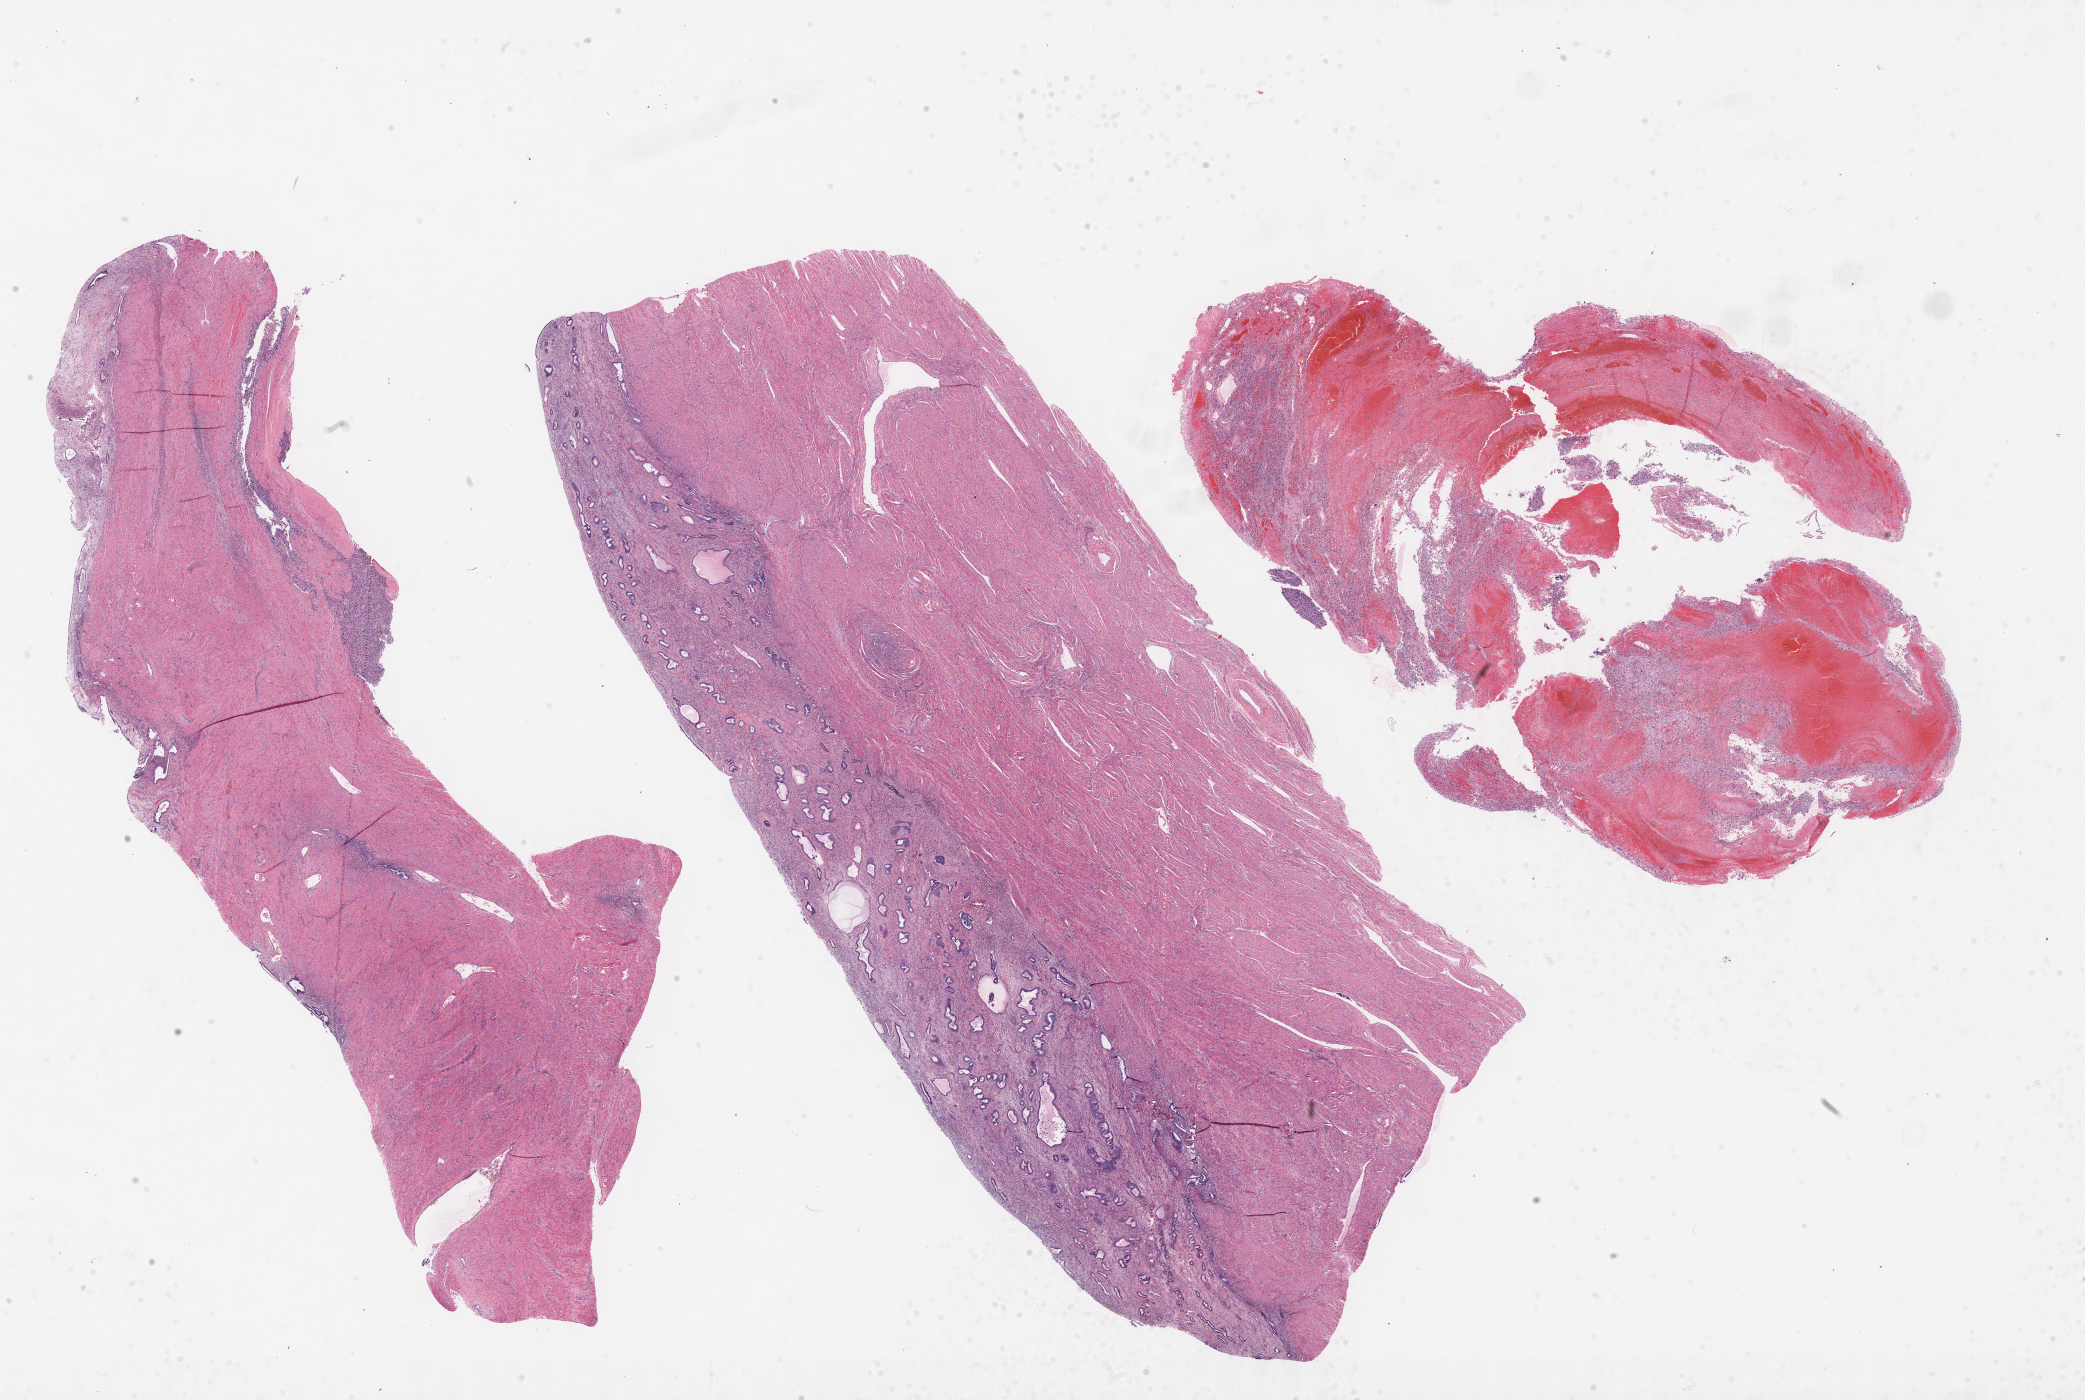
H&E-stained whole-slide image, low-resolution overview of the scanned area, about 33.7 x 22.6 mm; formalin-fixed paraffin-embedded (FFPE) diagnostic section; sample: primary tumour, corpus uteri. Female, age 55 years at initial diagnosis.
Pathologic diagnosis: Leiomyosarcoma, NOS (myometrium).